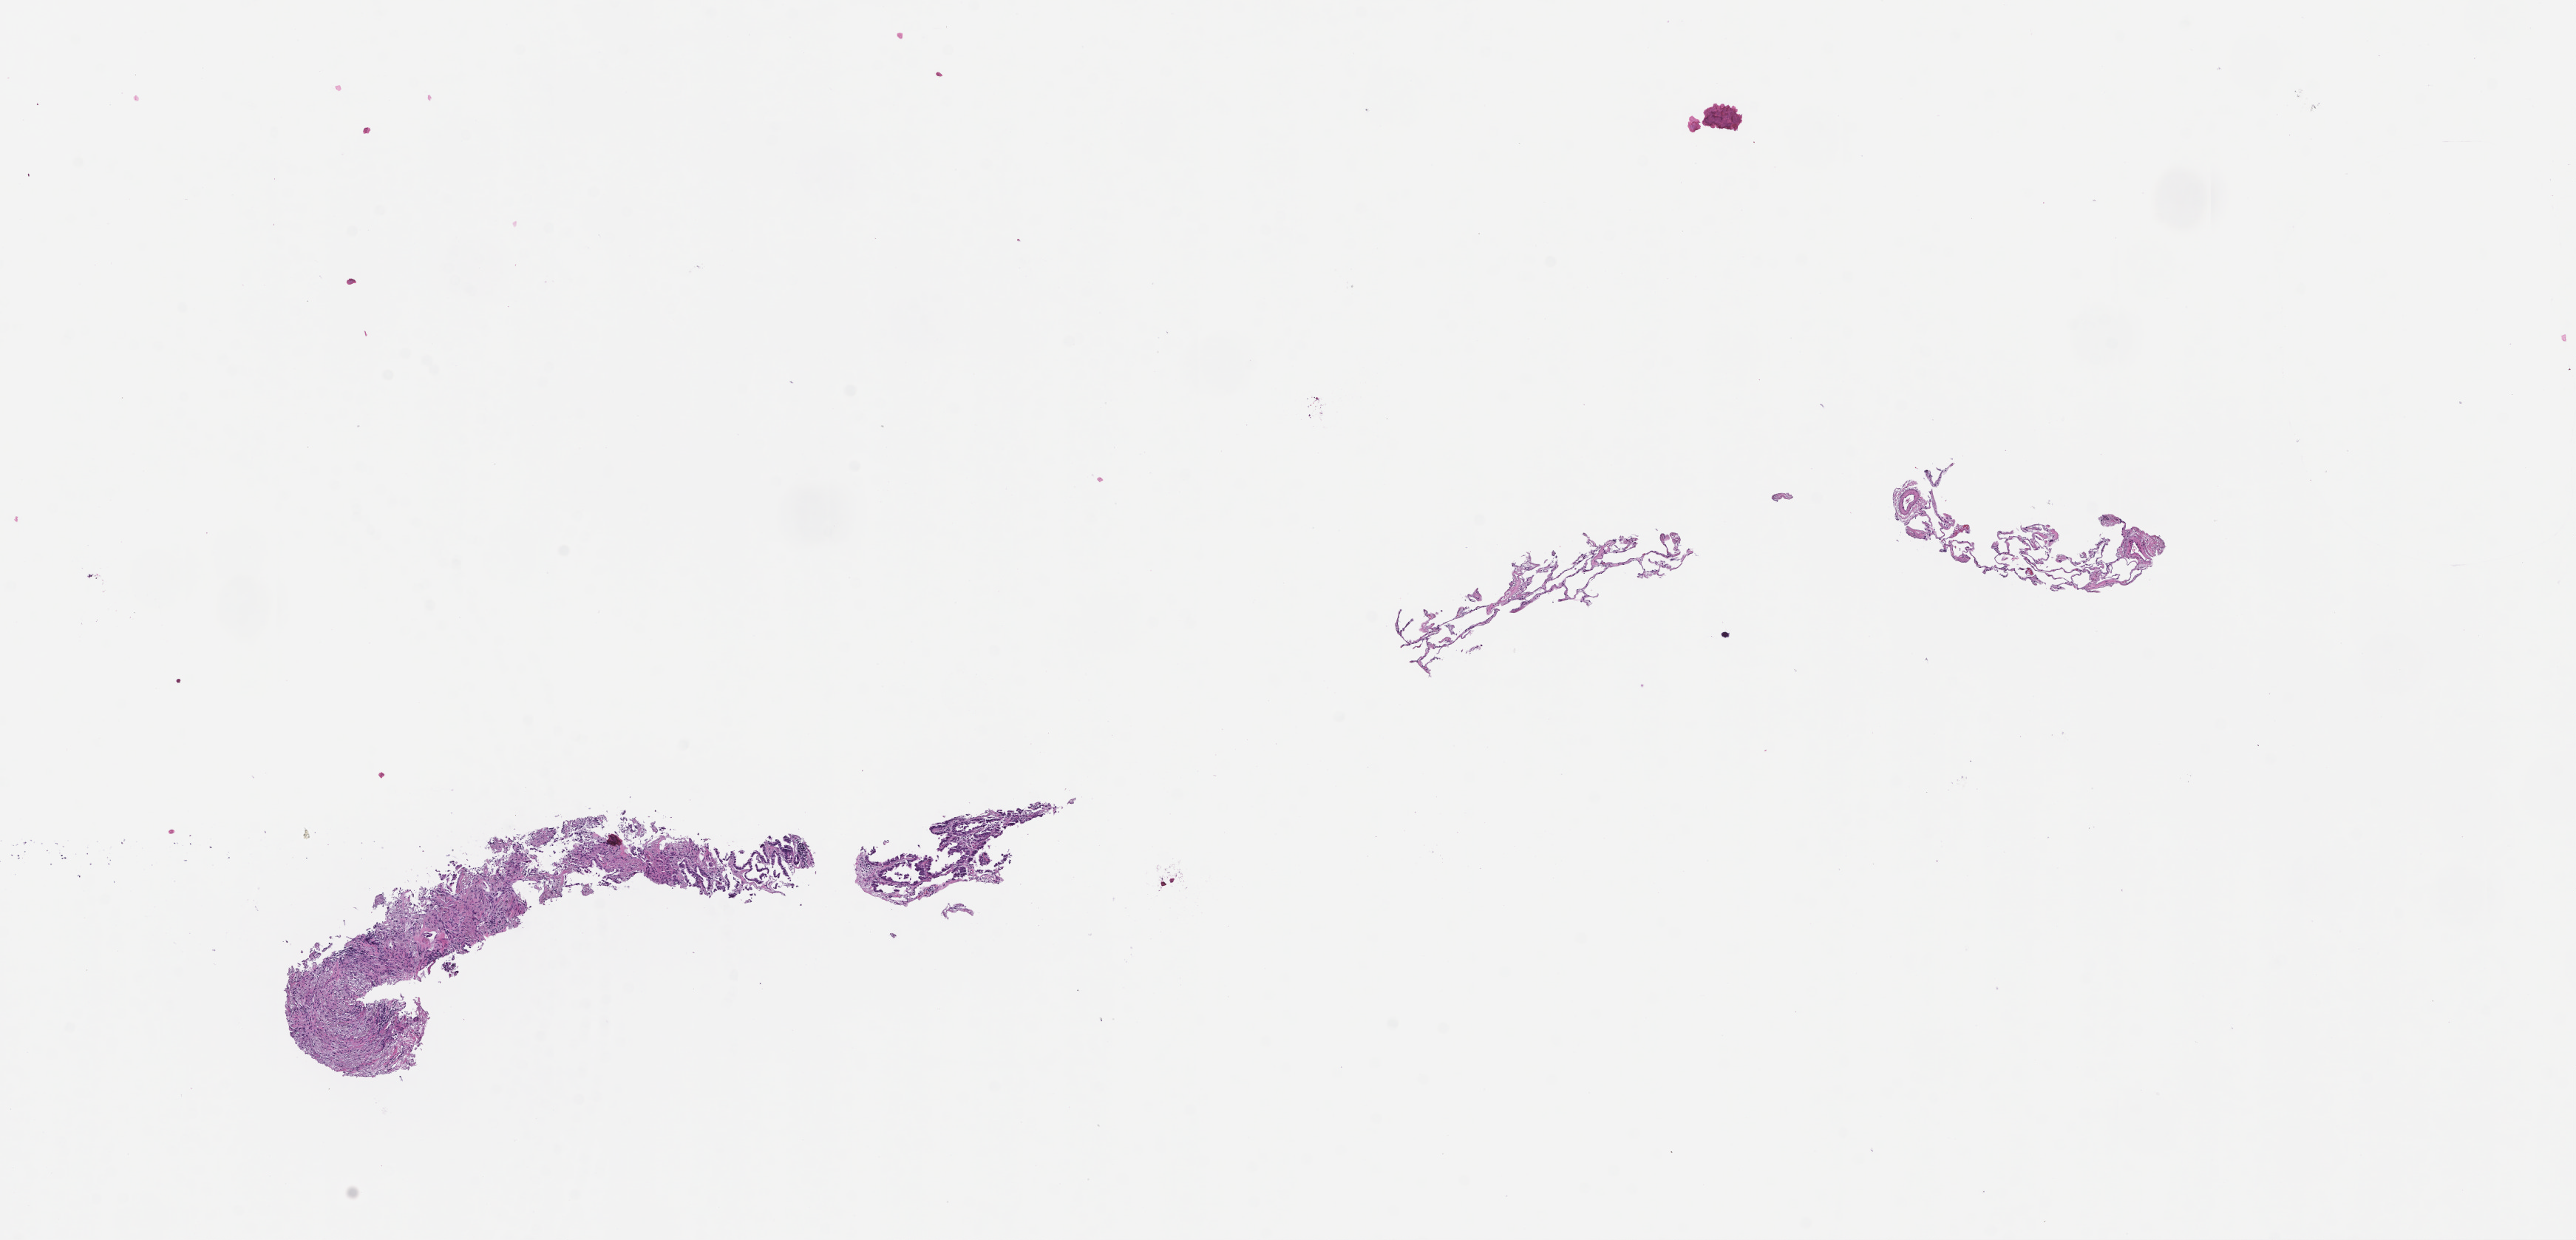
Whole-slide image, haematoxylin and eosin stain, low-resolution overview of the scanned area, about 14.1 x 6.8 mm. FFPE section. Site: lung. Specimen time point: collected at baseline (before treatment). Patient sex: female.
This section: primary tumor. Diagnosis: Non-Small Cell Lung Carcinoma.